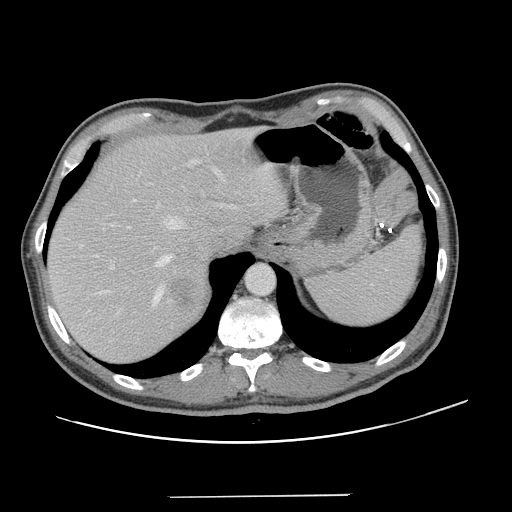
Contrast-enhanced abdominal CT, one axial slice; position 102 of 131 along the scan axis; intravenous contrast given; soft-tissue window (W 400 / L 40 HU); 512 × 512 image matrix. Male patient, age 60 years. From the clinical record (not read from this slice): diagnosis: colorectal cancer liver metastases, imaged before liver resection; multiple liver metastases: no; largest metastasis: 2.5 cm; disease in both lobes: no.
Annotated regions visible in this slice (expert manual segmentation):
- hepatic veins: bounding box <80,167,220,307> (left, top, right, bottom; pixels)
- liver: <47,129,284,363>
- planned liver remnant (the part of the liver to remain after resection): <47,128,284,351>
- portal vein (with intrahepatic branches): <93,157,260,270>
- liver metastasis: <171,278,198,312>